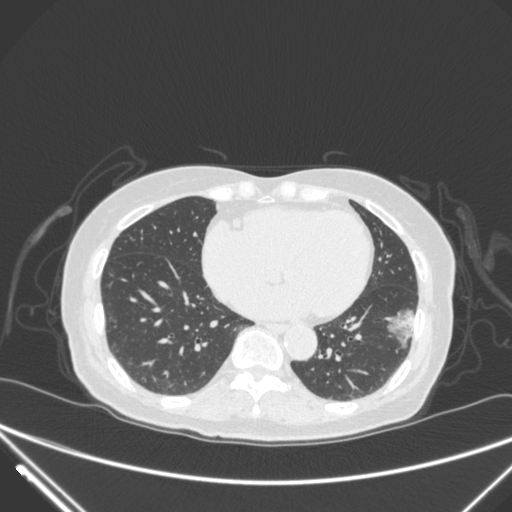
Chest CT, one axial slice. 120 kVp. Lung window (W 1500 / L -600 HU). 1 mm slice thickness. 512 × 512 image matrix. Female patient, age 82 years. Case-level facts recorded for this patient, not image findings: clinical TNM (as recorded): T1c N0 M0.
Outlined on this slice (bounding box drawn by a radiologist):
- lung tumour (recorded histology: adenocarcinoma): box from (x=383, y=291) to (x=425, y=354) px